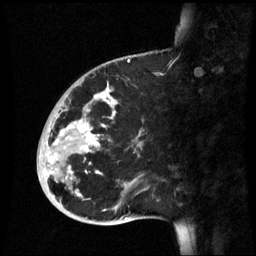
Breast MRI (dynamic contrast-enhanced), one sagittal slice. Position 20 of 60 along the scan axis. Dynamic contrast-enhanced series, image 2 of 3 at this slice position (ordered by acquisition). 1.5 T. TE 4.2 ms, TR 8.9 ms. 256 × 256 image matrix, field of view 220 × 220 mm. Female patient, age 35 years. Case-level facts recorded for this patient, not image findings: setting: breast cancer imaged before/during neoadjuvant chemotherapy; receptor status: HR-positive, HER2-negative.
Outlined on this slice (semi-automatic segmentation, software-assisted and operator-edited):
- analysis volume of interest (the breast-tissue region the enhancement analysis was run in; not a lesion): bounding box <37,74,159,221> (left, top, right, bottom; pixels)
- tumour enhancement mask (voxels above the 70 % enhancement threshold inside the analysis volume of interest): <44,88,117,195>